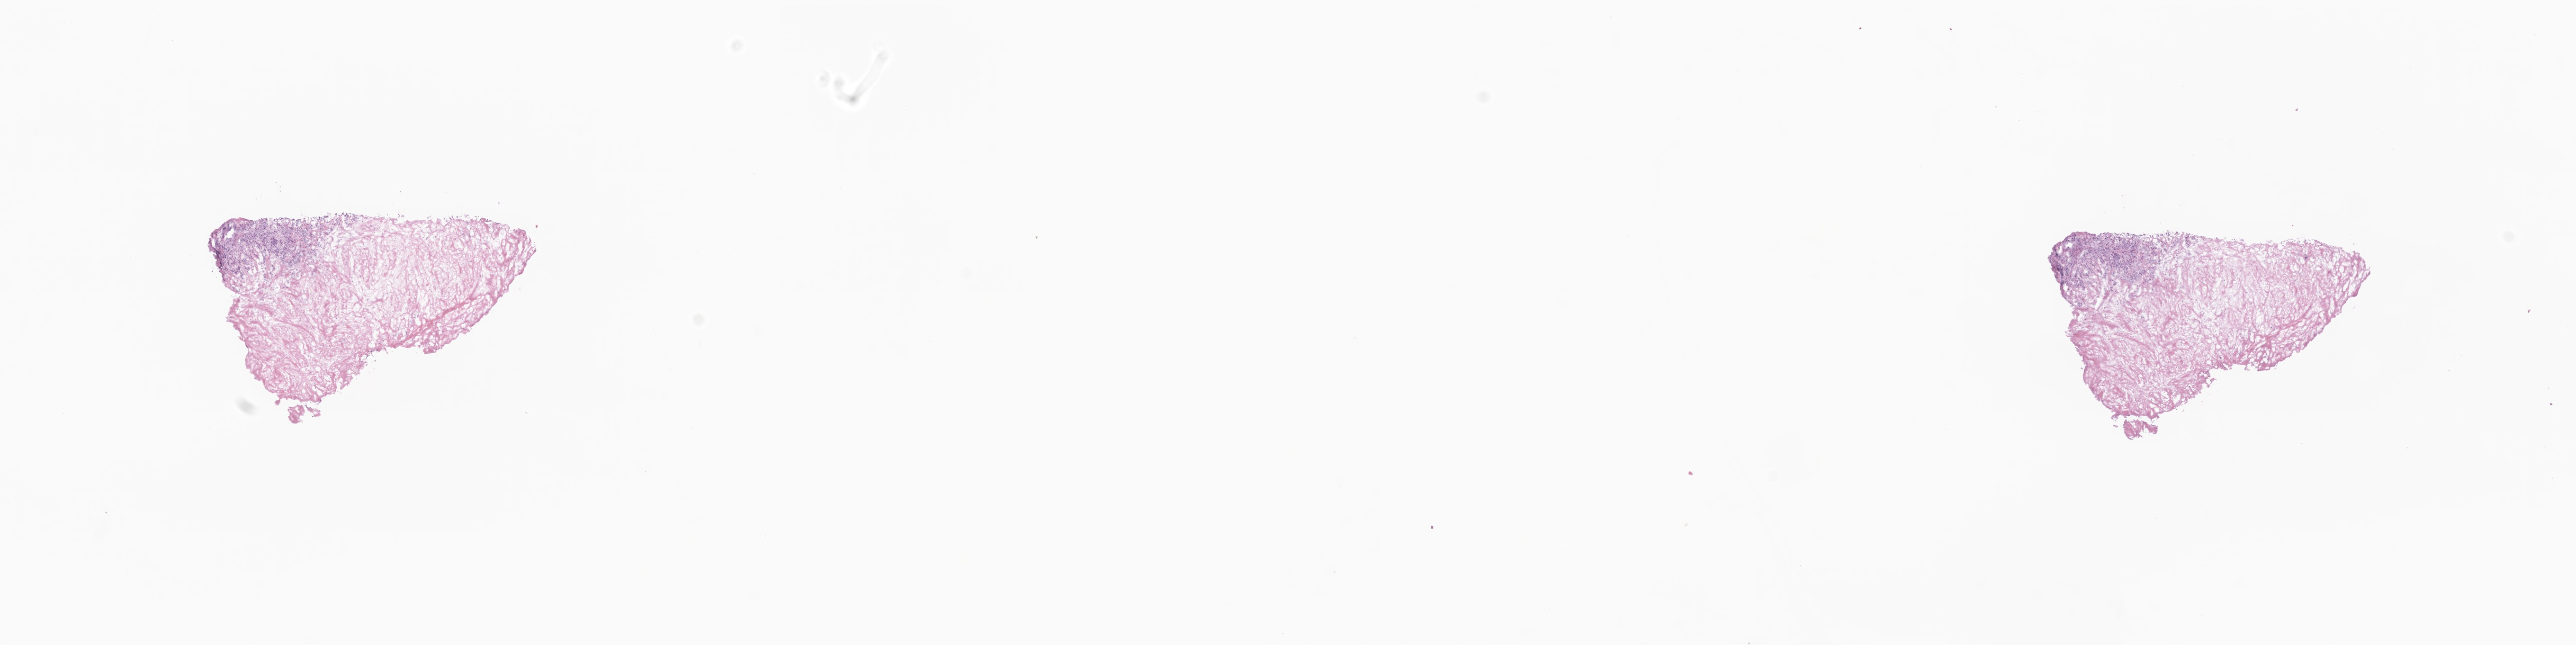
Whole-slide image, H&E stain, shown as a low-resolution overview of the whole scanned area (about 22.9 x 5.7 mm); cryosection; specimen: primary tumor; site: breast (left). Female patient; age at initial diagnosis 81 years. Pathologist review of this section (percent, as recorded): tumor cells 28%, tumor nuclei 62%.
Diagnosis: Infiltrating duct carcinoma, NOS.